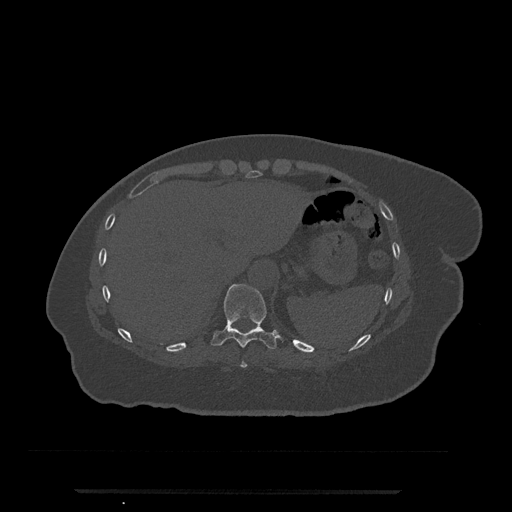
CT including the spine, one axial slice. Slice 287 of 797 in the series (ordered by position). Bone window (W 1800 / L 400 HU). 512 × 512 image matrix, field of view 440 × 440 mm. Patient: female, 51 years. Case-level facts recorded for this patient, not image findings: primary cancer: neuro.
Structures marked on this image (semi-automatically segmented with operator editing):
- T10 vertebra: bounding box [x1, y1, x2, y2] px = [211, 284, 279, 349]
- T9 vertebra: [241, 361, 247, 368]